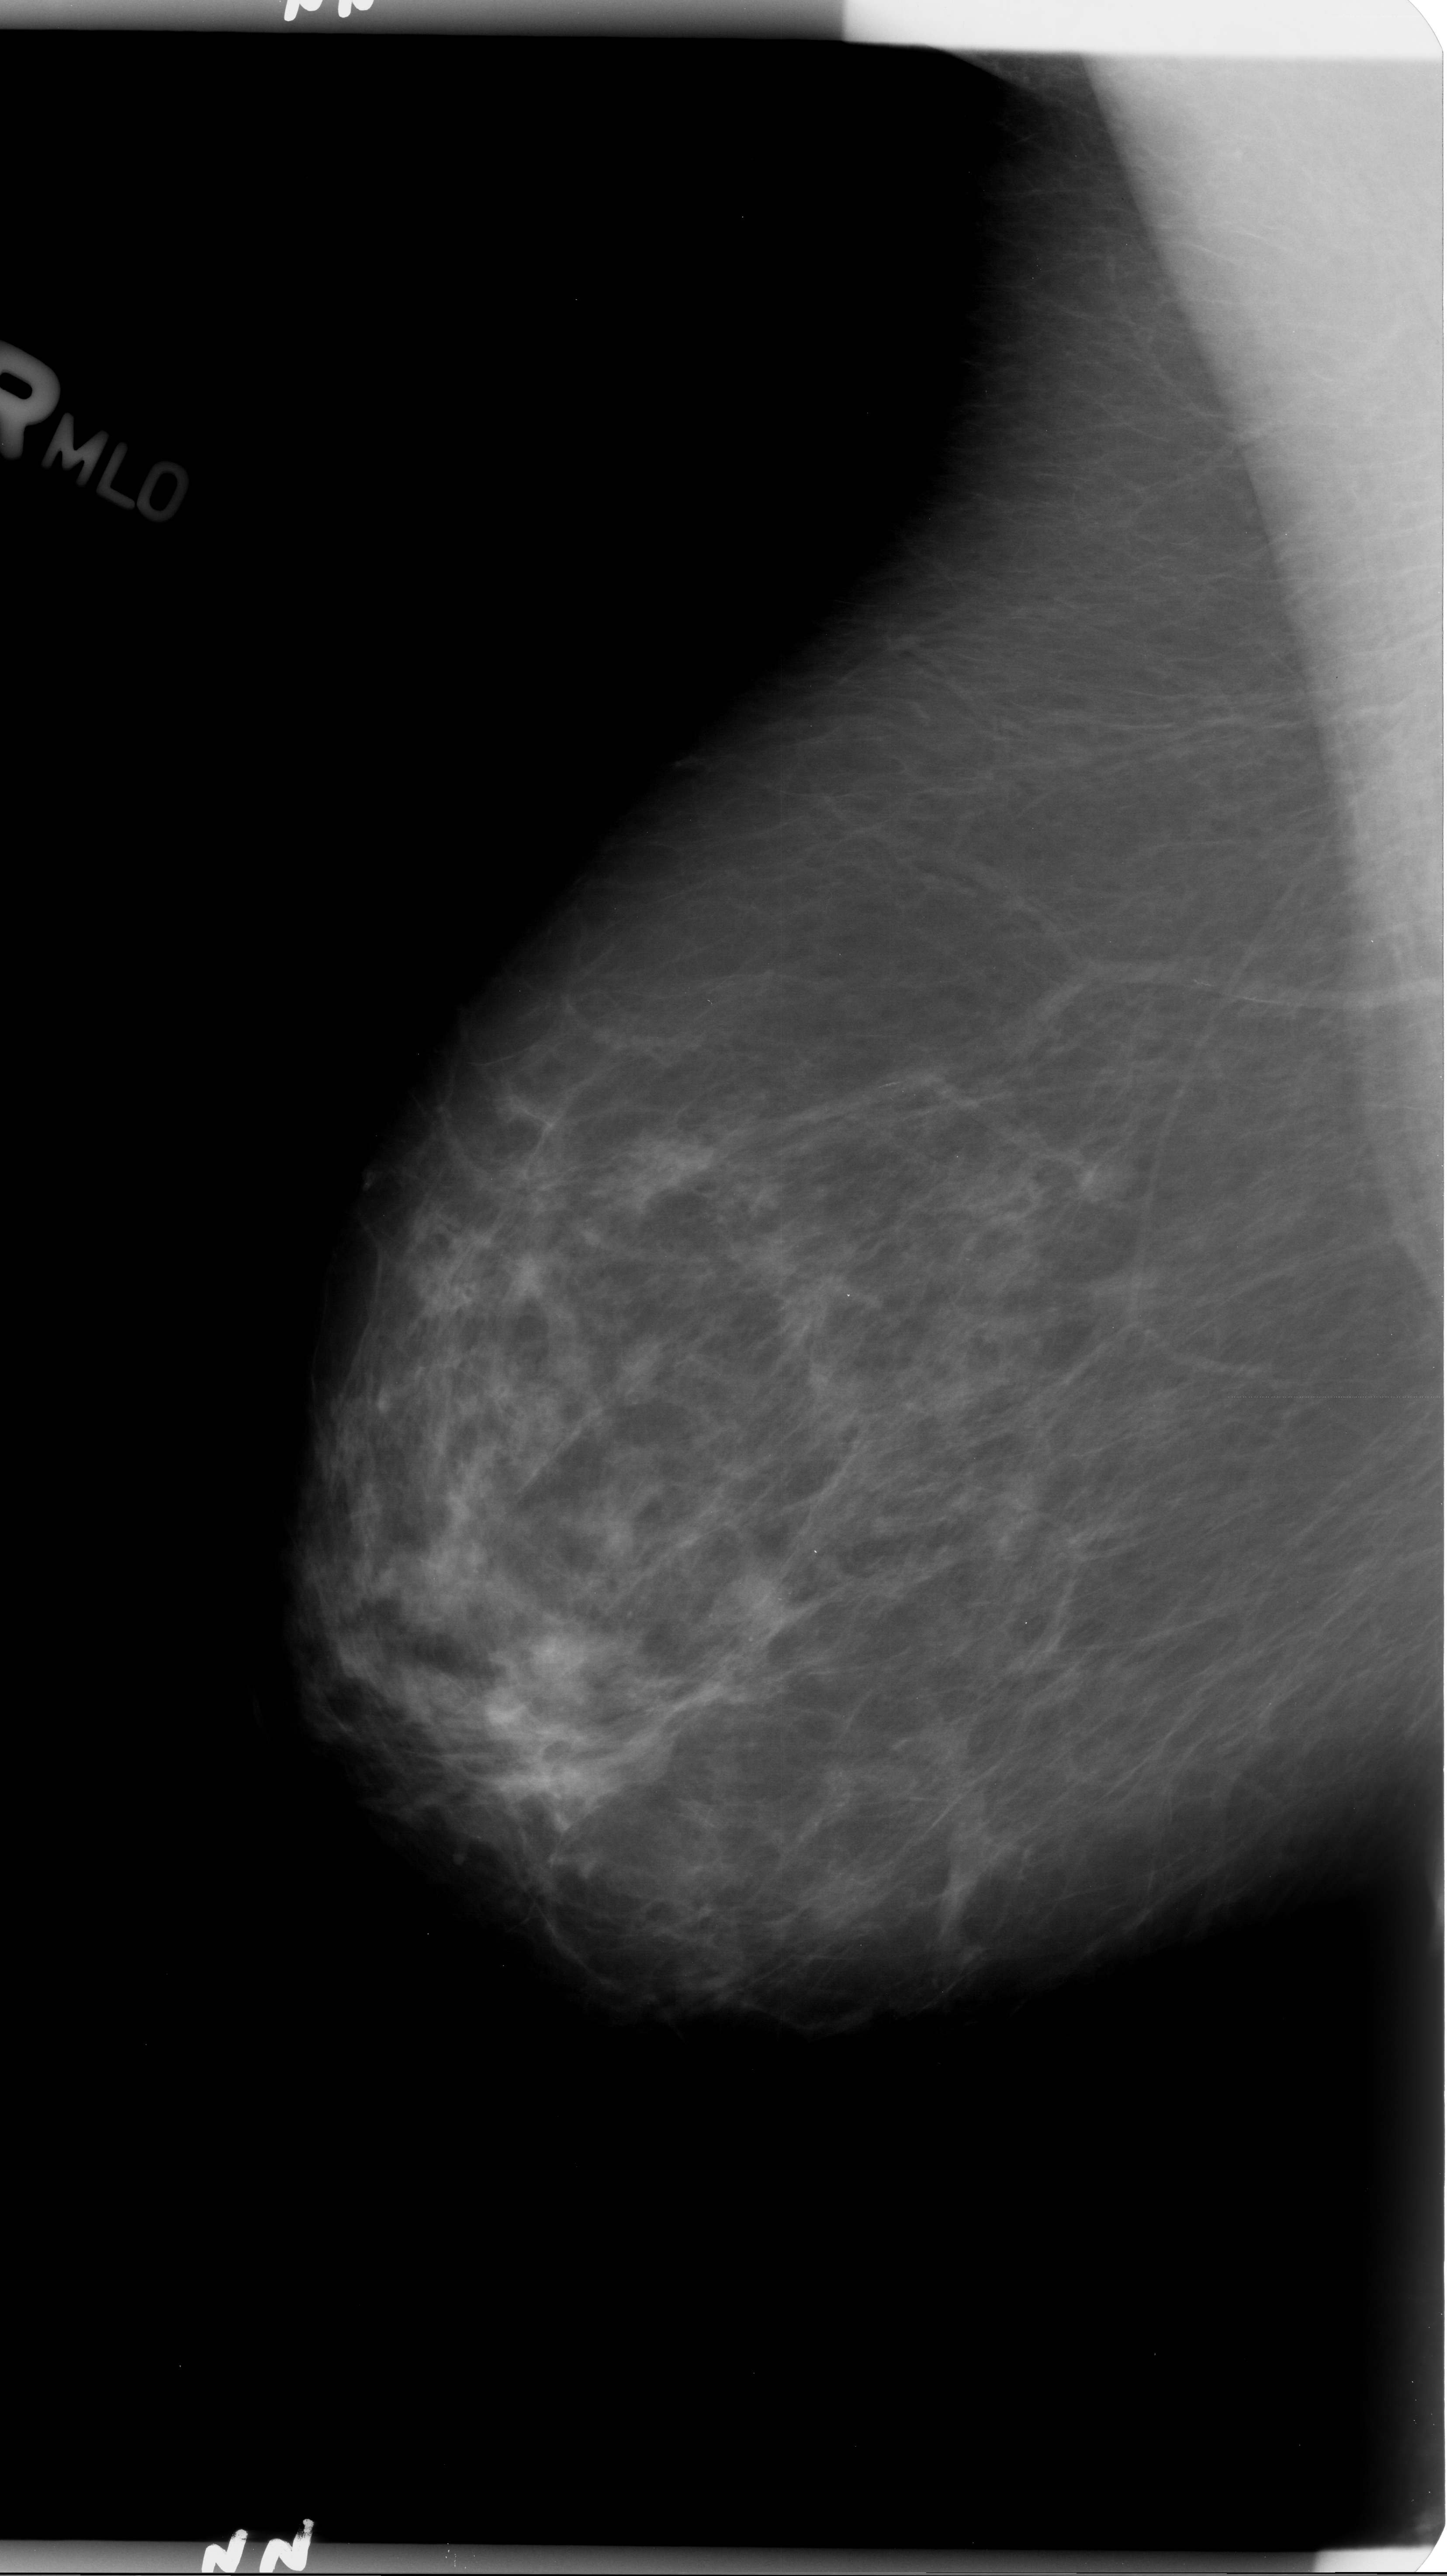
Digitized screen-film mammogram, right breast, MLO view, breast composition: scattered fibroglandular densities (BI-RADS density category 2 of 4).
Marked findings (only marked abnormalities are described; nothing is implied about the rest of the image): calcifications, morphology punctate / pleomorphic, distribution clustered; BI-RADS assessment category 3; subtlety rating 3 on a 1 (subtle) to 5 (obvious) scale; pathology result (as recorded, not read from the image): benign.